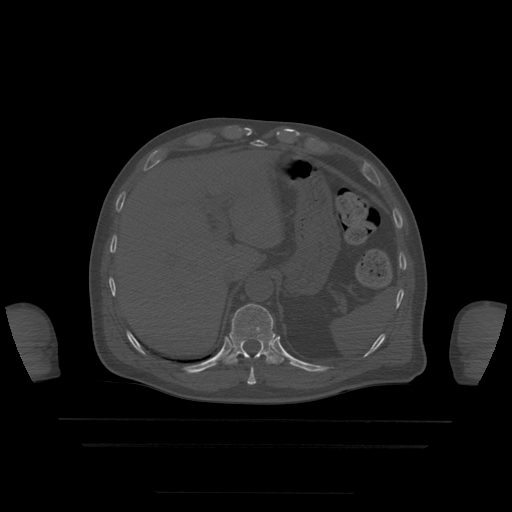
CT including the spine, one axial slice; slice 226 of 522 in the series (ordered by position); bone window (W 1800 / L 400 HU); 1.25 mm slice thickness; 512 × 512 image matrix, field of view 436 × 436 mm. Patient age 68 years. From the clinical record (not read from this slice): primary cancer: urothelial.
Structures marked on this image (semi-automatic segmentation, software-assisted and operator-edited):
- T10 vertebra: bounding box [x1, y1, x2, y2] px = [247, 359, 270, 385]
- T11 vertebra: [223, 304, 284, 365]